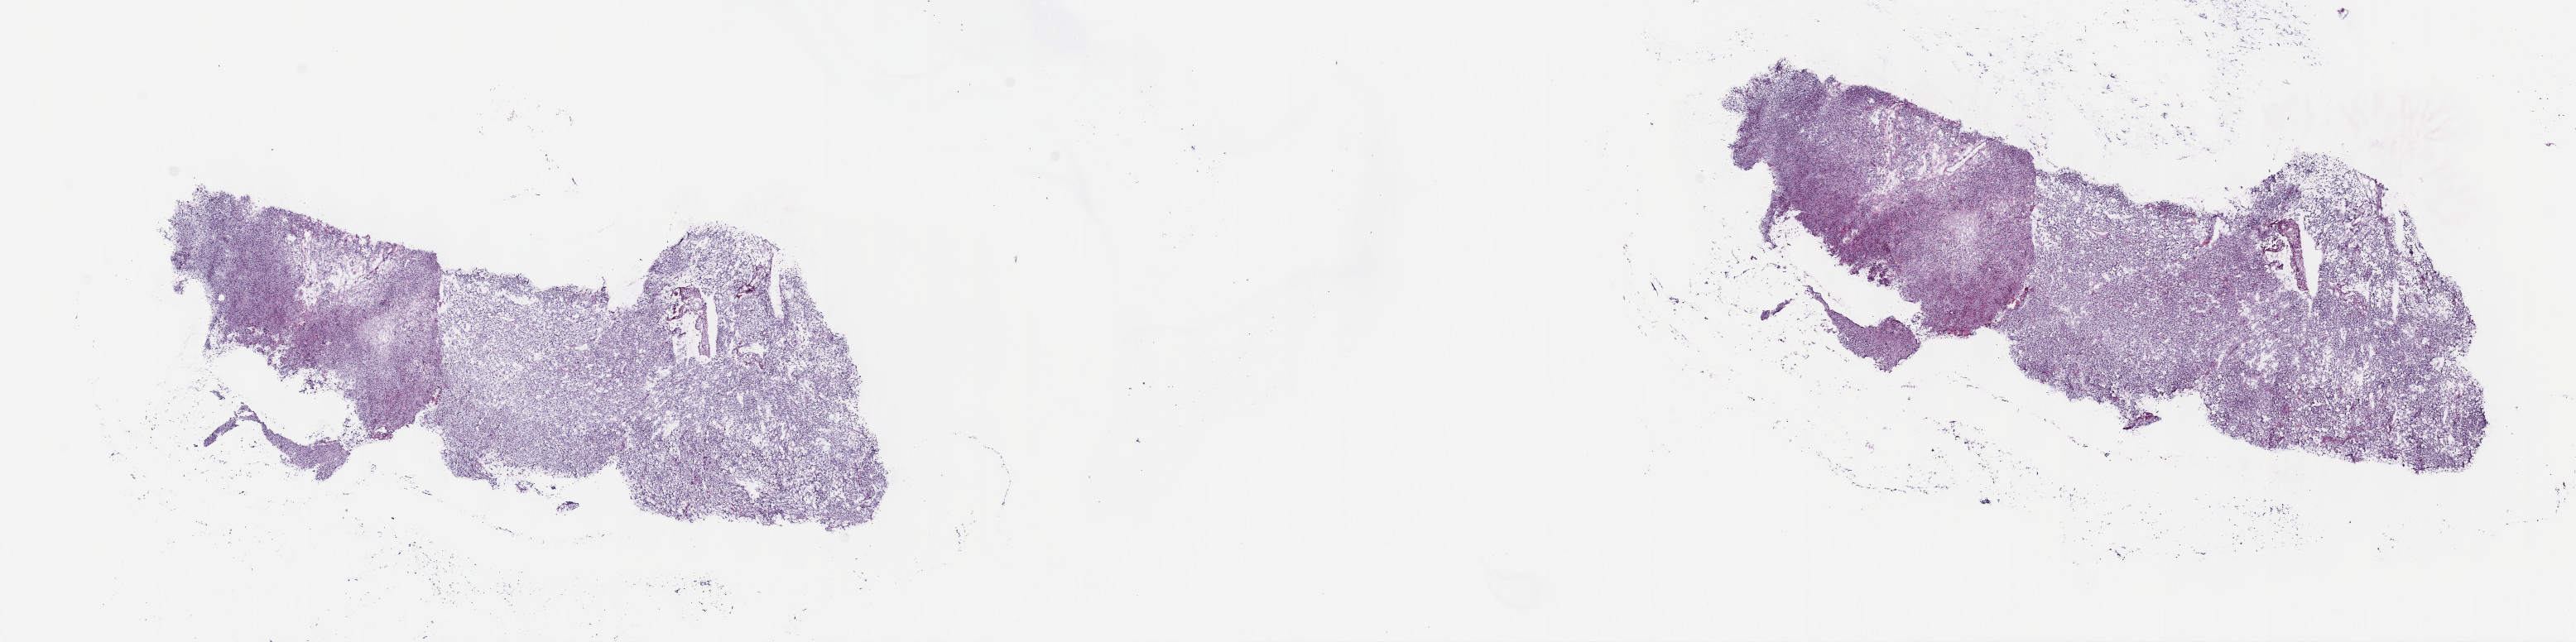
Digitized Hematoxylin and eosin (H&E) stained tissue section (whole slide) — low-resolution overview of the scanned area, about 25.2 x 6.3 mm (slide scanned at 40x); frozen section from the top of the tissue portion; brain, primary tumour sample. Patient: male, age at initial diagnosis 47 years. Histologic grade: G3 (poorly differentiated). Slide review estimates, as recorded: tumour cells 55%, tumour nuclei 90%, normal cells 10%, stromal cells 35%, necrosis 0%. Inflammatory infiltration, as recorded: lymphocyte infiltration 0%, monocyte infiltration 0%, neutrophil infiltration 0%.
Diagnosis: Oligodendroglioma, anaplastic (cerebrum). Laterality: left.